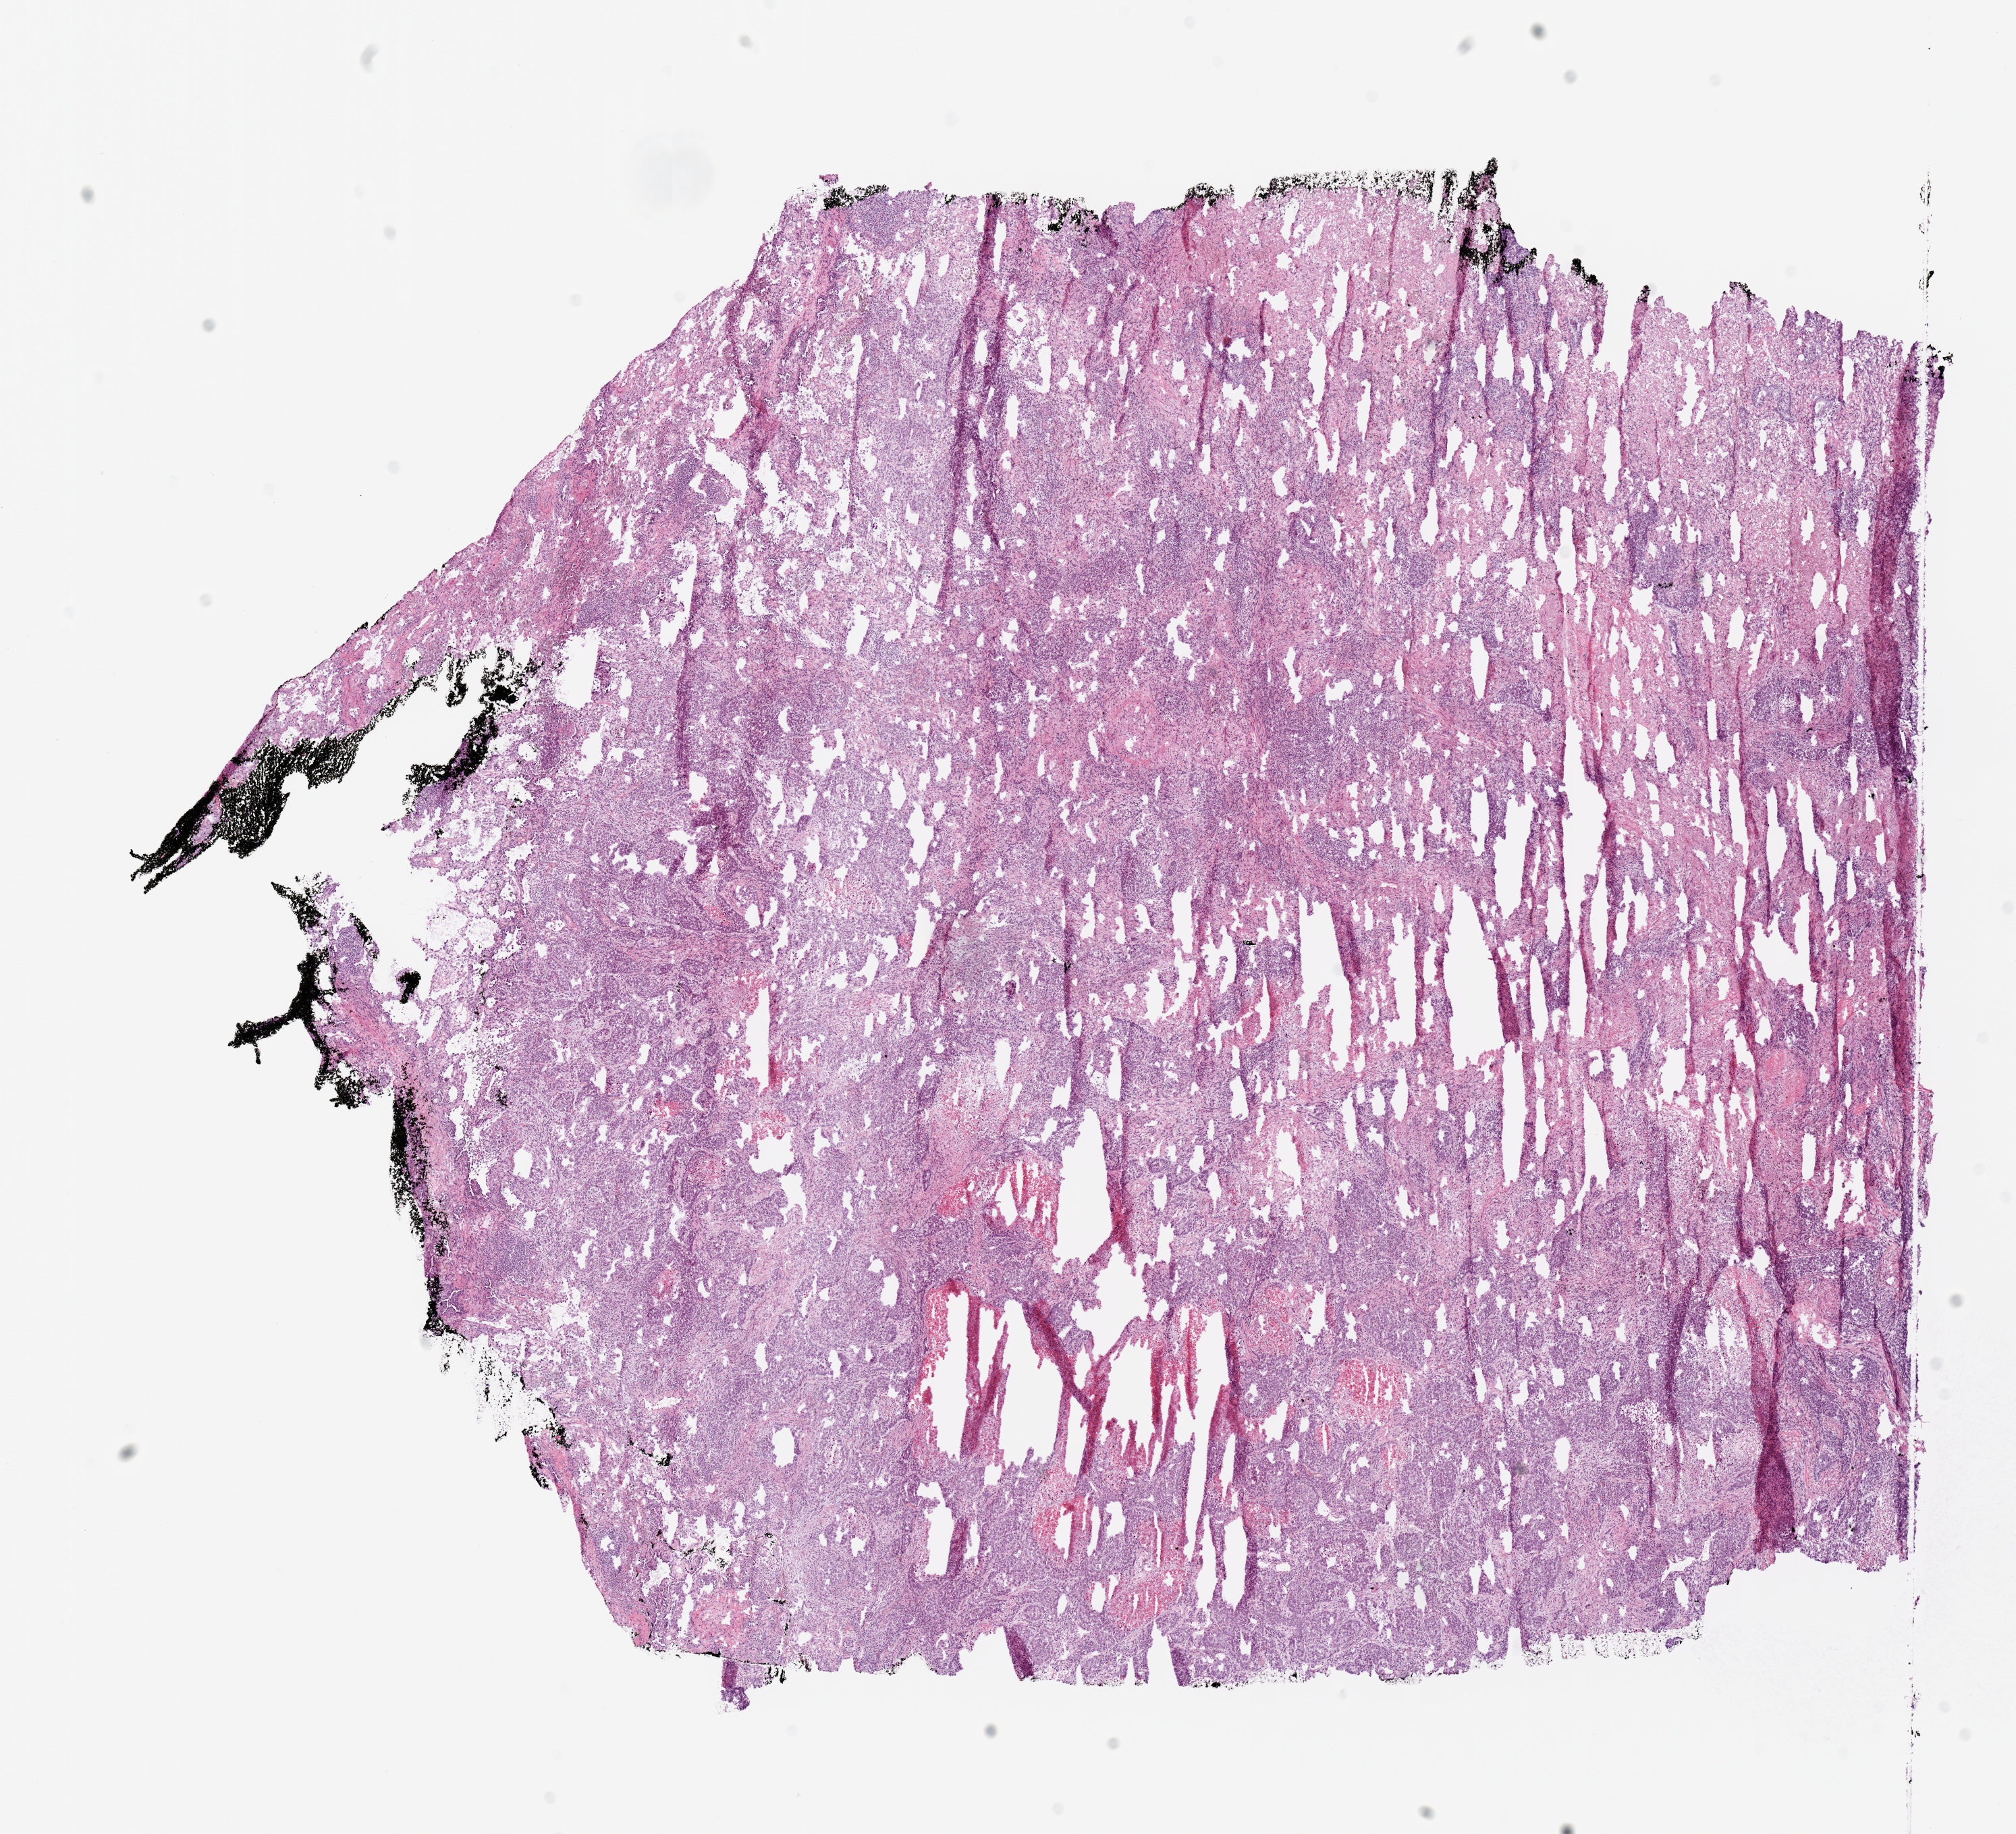
H&E-stained whole-slide image, low-resolution overview of the scanned area, about 11.8 x 10.7 mm; frozen section from the top of the tissue portion; primary tumour sample from the lung. Patient: male, age at initial diagnosis 52 years. Pathologist review of this section (percent, as recorded): tumour cells 93%, tumour nuclei 80%, normal cells 0%, stromal cells 0%, necrosis 7%. Inflammatory infiltration, as recorded: lymphocyte infiltration 15%.
AJCC pathologic stage: IB (6th edition). Laterality: left. TNM: T2 N0 M0. Pathologic diagnosis: Adenocarcinoma, NOS (upper lobe, lung).